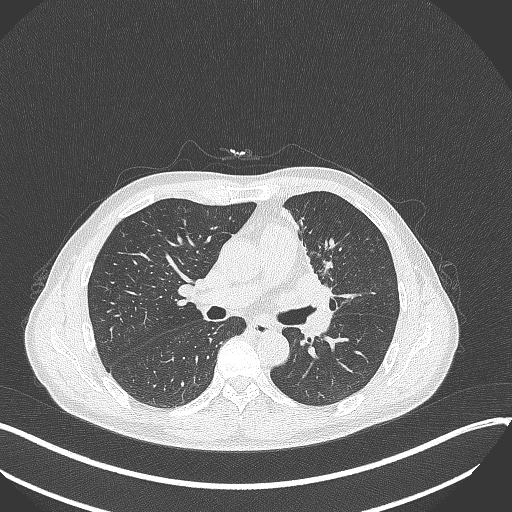
Chest CT, one axial slice. Position 188 of 411 along the scan axis. Reconstruction kernel B70f. 120 kVp. Lung window (W 1500 / L -600 HU). 512 × 512 image matrix, field of view 400 × 400 mm. Male patient, age 56 years. Case-level facts recorded for this patient, not image findings: clinical TNM (as recorded): T2a N0 M0.
Annotated regions visible in this slice (bounding box drawn by a radiologist):
- lung tumour (recorded histology: squamous cell carcinoma): box from (x=269, y=270) to (x=342, y=316) px